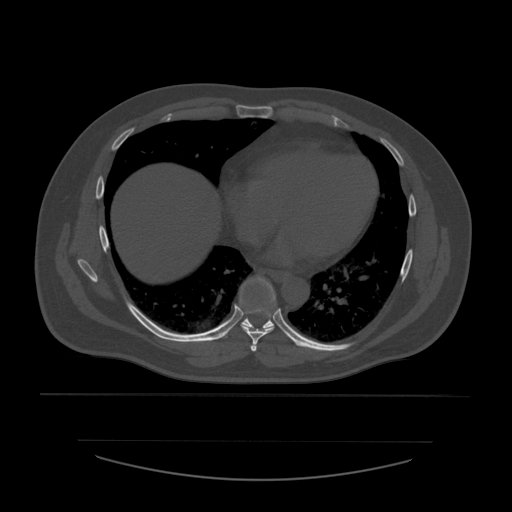
CT including the spine, one axial slice. Position 350 of 532 along the scan axis. Reconstruction kernel STANDARD. 120 kVp. Bone window (W 1800 / L 400 HU). 1.25 mm slice thickness. 512 × 512 image matrix, field of view 441 × 441 mm. Patient age 44 years. Case-level facts recorded for this patient, not image findings: primary cancer: soft tissue sarcoma.
Structures marked on this image (semi-automatically segmented with operator editing):
- T6 vertebra: bounding box (x1, y1, x2, y2) in pixels: (250, 279, 262, 353)
- T7 vertebra: (240, 283, 276, 344)
- T8 vertebra: (241, 278, 276, 332)